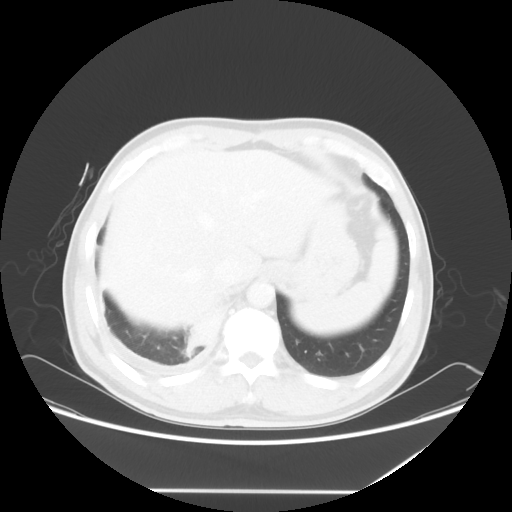
Chest CT, one axial slice. Position 12 of 60 along the scan axis. Reconstruction kernel STANDARD. Lung window (W 1500 / L -600 HU). 5 mm slice thickness. 512 × 512 image matrix, field of view 419 × 419 mm. Patient: male, 48 years. Case-level facts recorded for this patient, not image findings: clinical TNM (as recorded): T3 N3 M1a.
Annotated regions visible in this slice (rectangle marked by the reading radiologist):
- lung tumour (recorded histology: squamous cell carcinoma): bounding box [x1, y1, x2, y2] px = [180, 296, 229, 361]